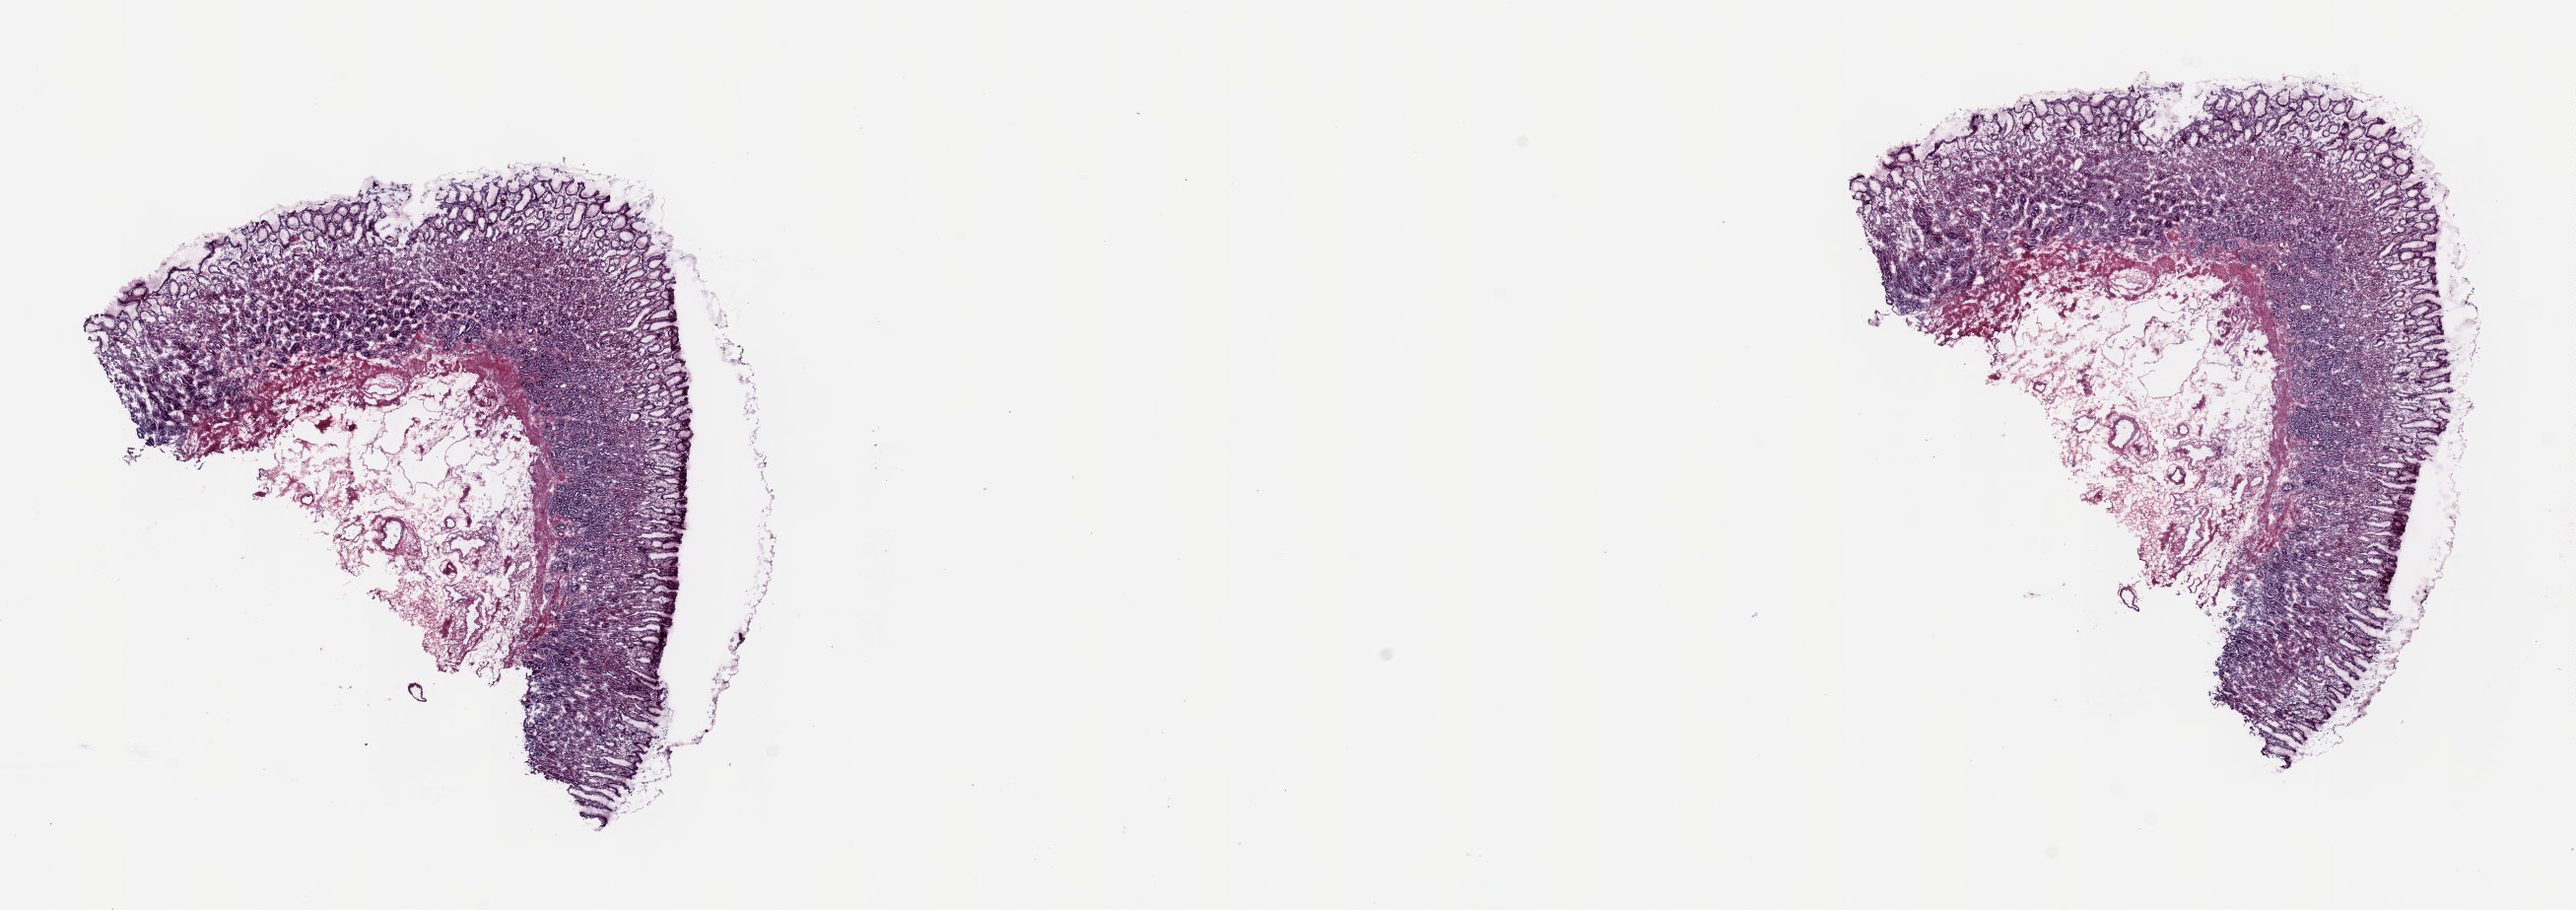
Whole-slide histology image, H&E — shown as a low-resolution overview of the whole scanned area (about 20.7 x 7.3 mm, slide scanned at 20x). Frozen section. Esophagus, solid tissue normal (non-tumour tissue) sample. Male patient. Slide review estimates, as recorded: tumour cells 0%, tumour nuclei 0%, normal cells 100%, stromal cells 0%, necrosis 0%. Infiltration values recorded for this section: lymphocyte infiltration 1%, monocyte infiltration 0%, neutrophil infiltration 0%.
This section: solid tissue normal sample (biorepository sample class). Patient diagnosis: Squamous cell carcinoma, NOS (middle third of esophagus).